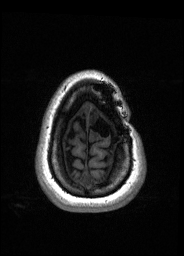
Pre-operative brain MRI before brain-tumour surgery, one axial slice; T1-weighted post-contrast; 1 mm slice thickness; 184 × 256 image matrix. Case-level facts recorded for this patient, not image findings: histopathology: Oligodendroglioma; WHO grade: 2; IDH mutation: yes; tumour location: Left Frontal.
Structures marked on this image (expert manual segmentation):
- tumour: bounding box <88,110,99,125> (left, top, right, bottom; pixels)